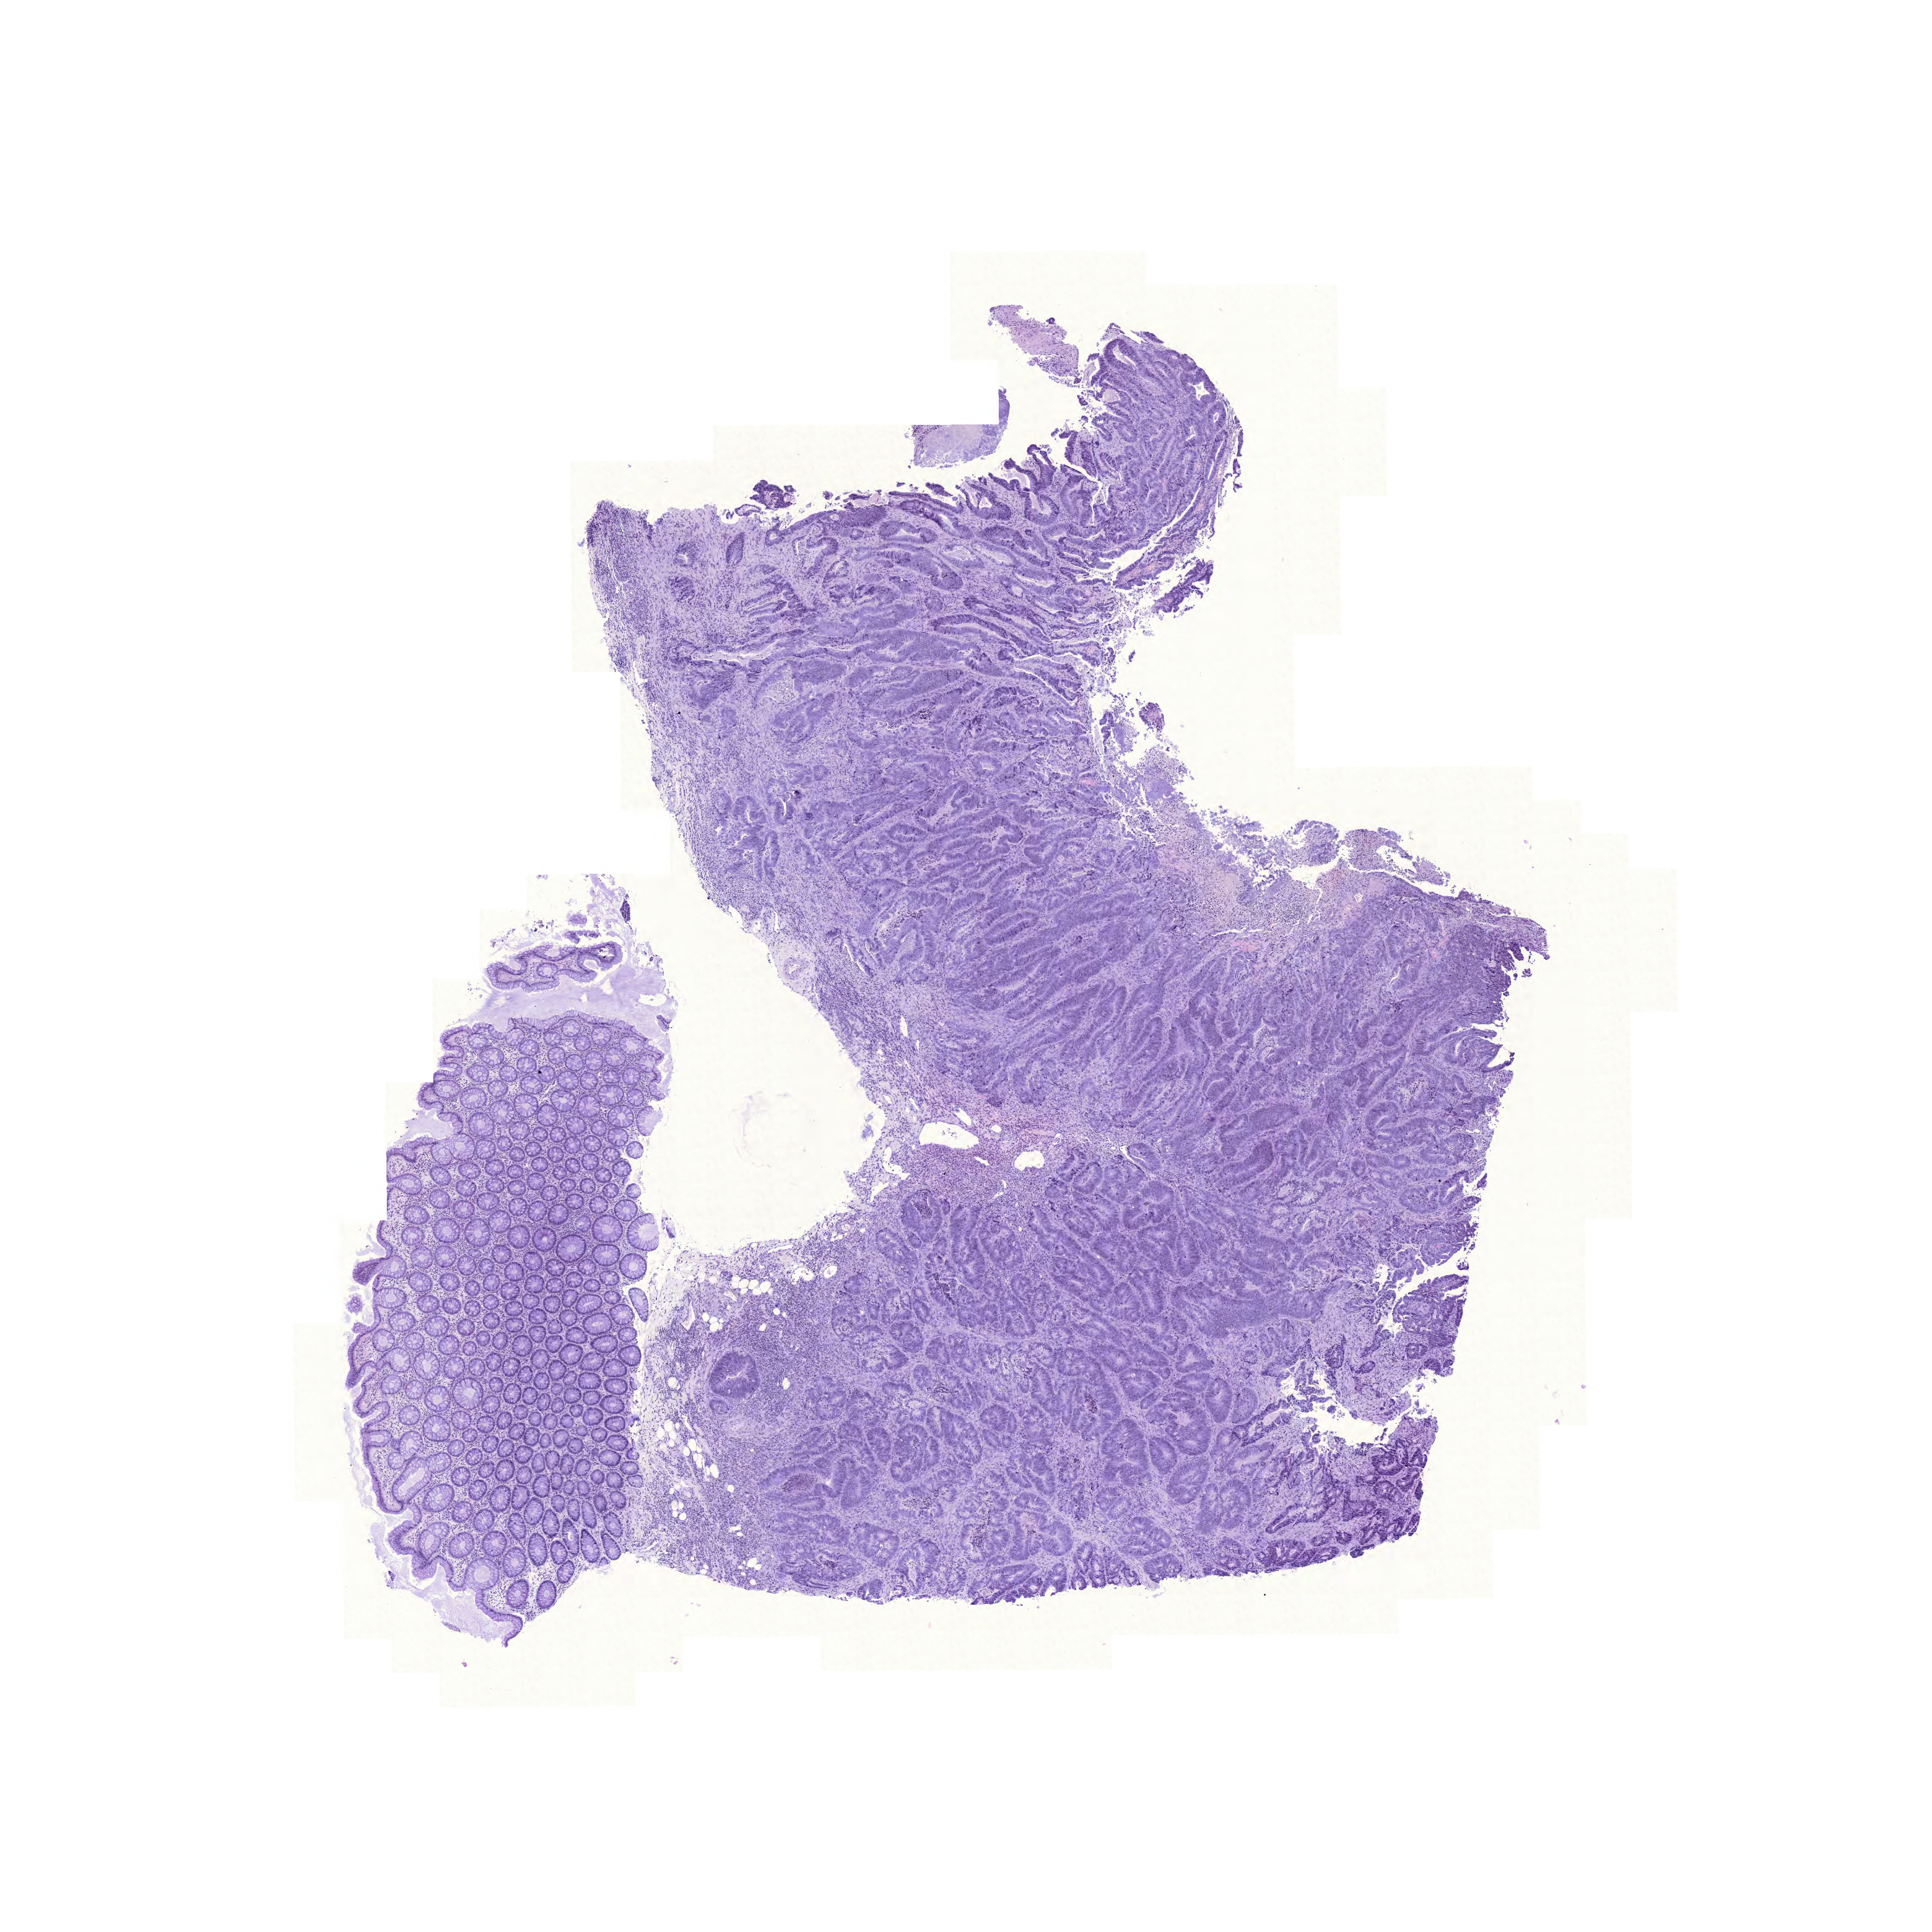
Digitized H&E tissue section (whole slide) — low-resolution overview of the scanned area, about 11.6 x 11.6 mm (slide scanned at 20x); formalin-fixed paraffin-embedded (FFPE) diagnostic section; primary tumour sample from the colon. Patient: male, age at initial diagnosis 85 years.
• lymph nodes positive (case pathology): 0 of 28 examined
• AJCC pathologic stage: II
• diagnosis: Adenocarcinoma, NOS (sigmoid colon)